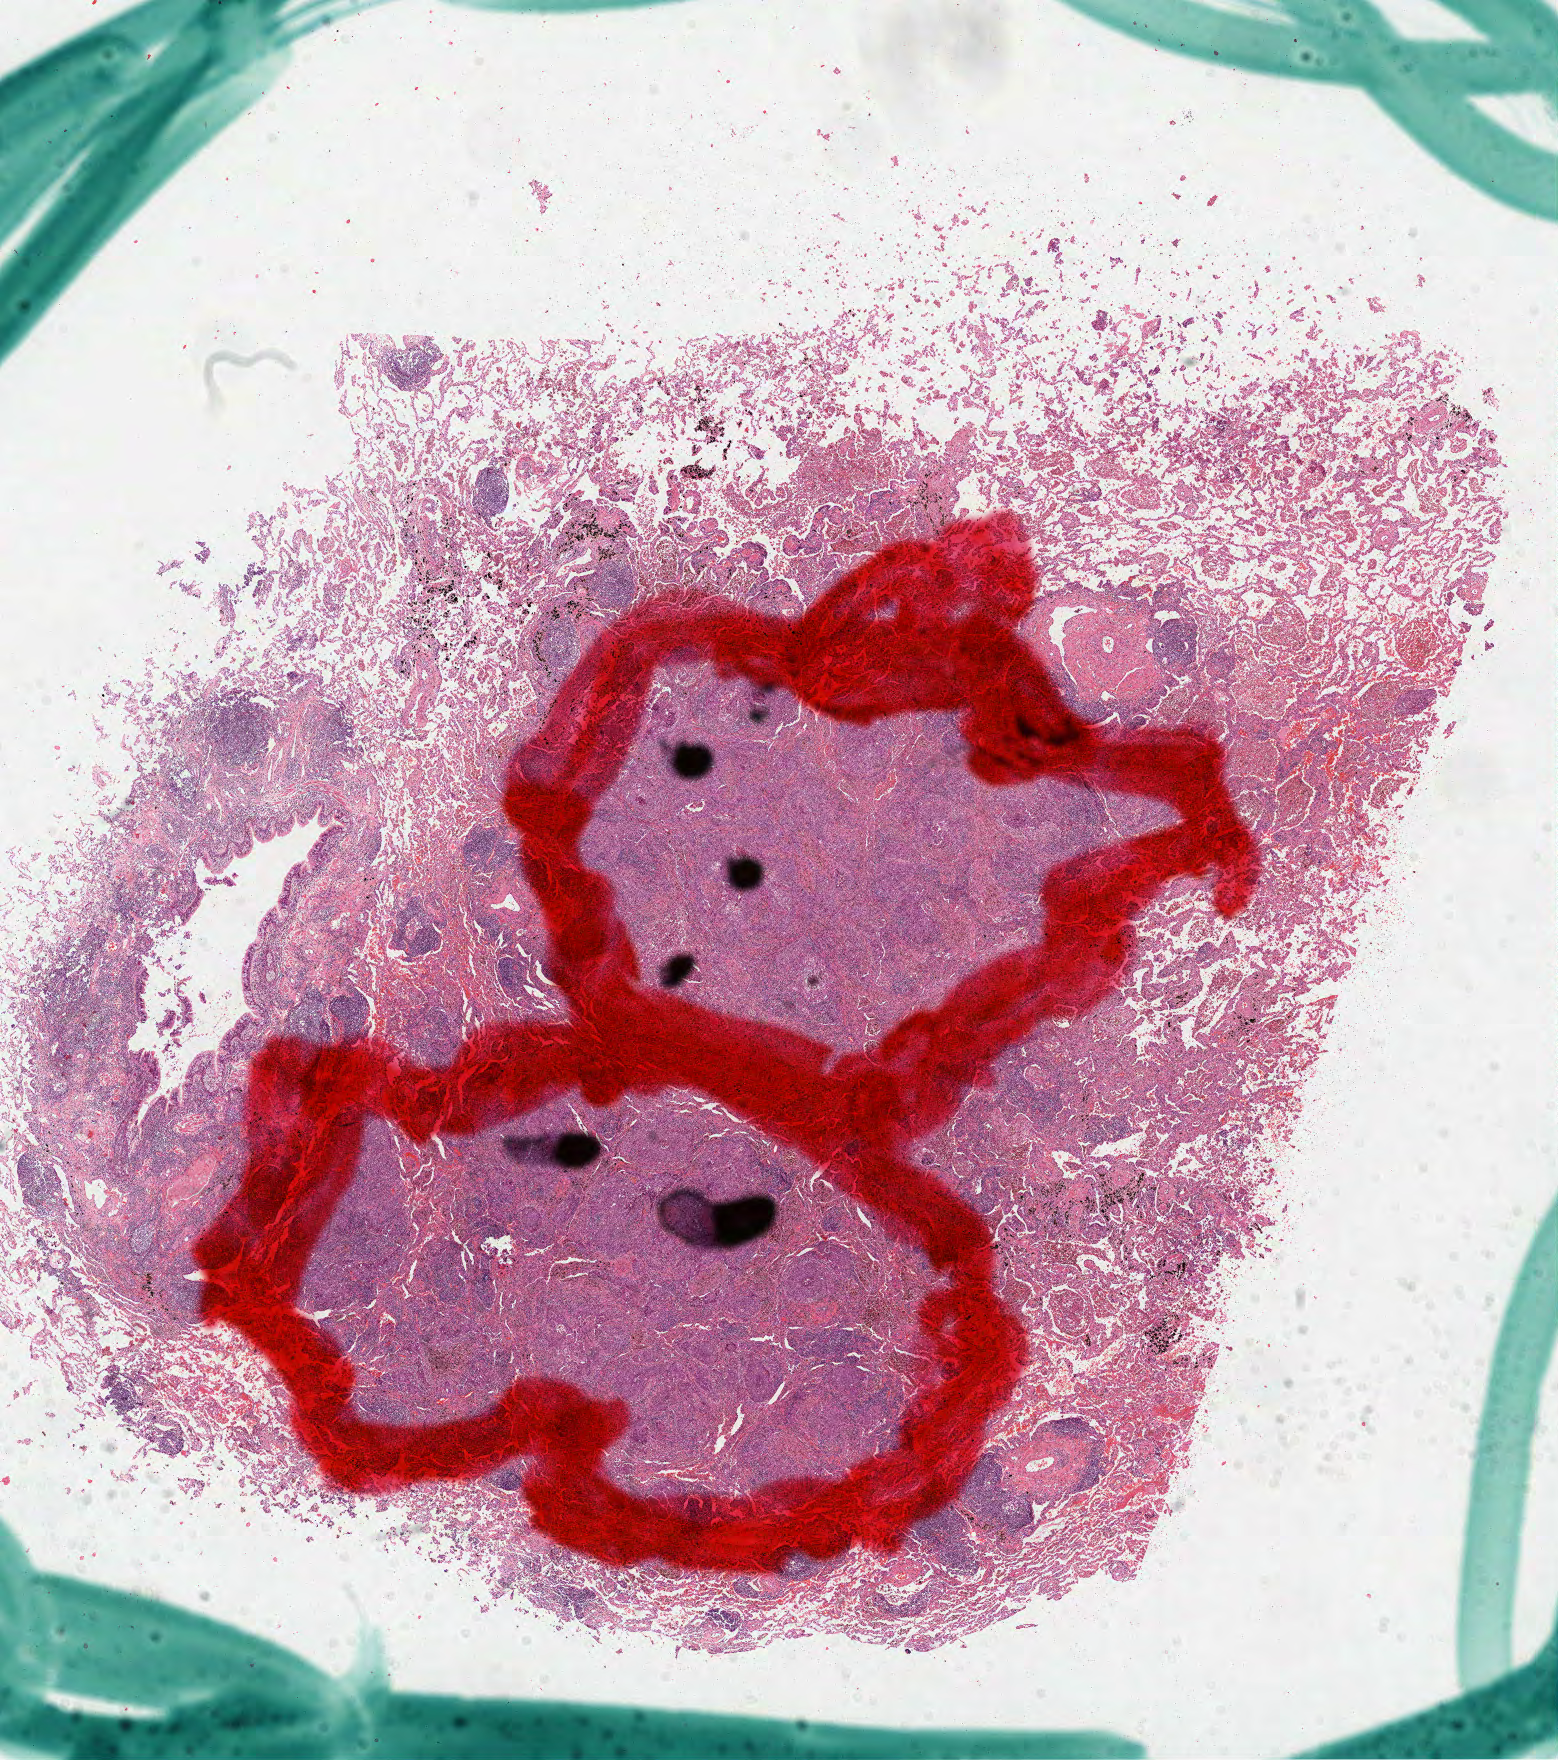
Digitized Hematoxylin and eosin (H&E) stained tissue section (whole slide) — whole scanned area (about 12.6 x 14.2 mm, acquisition: 40x scan) shown as a low-resolution overview; FFPE section; primary tumour sample from the lung. Male patient; age at initial diagnosis 62 years.
AJCC pathologic stage: IA (7th edition). Histologic diagnosis: Squamous cell carcinoma, NOS (lower lobe, lung).